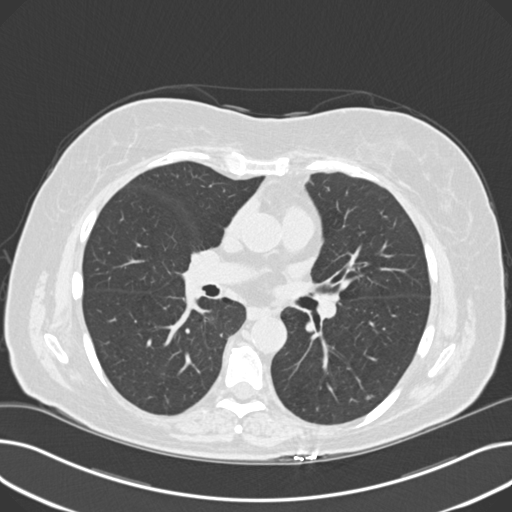
Low-dose screening chest CT, axial slice, third annual screen, lung window (W 1500 / L -600 HU), 2 mm slice thickness. Female, age 60 years at enrolment. Current smoker at enrolment.
Expert-annotated lung lesion, bounding box (x1, y1, x2, y2) in pixels: (349, 263, 391, 304). The screening reader recorded 8 non-calcified nodules or masses ≥4 mm on this exam (right upper lobe, lingula, lingula, right middle lobe, right lower lobe, left lower lobe, left lower lobe, left lower lobe); which of them this box marks is not recorded. Participant outcome: lung cancer diagnosed 176 days after this screen — non-small cell carcinoma, left upper lobe, poorly differentiated (G3), stage IB (AJCC 6th edition), 7 mm at pathology.